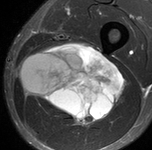
MRI of an extremity soft-tissue mass, one axial slice; position 53 of 90 along the scan axis; STIR; MR volume resampled by the dataset authors to the PET/CT grid (not the native acquisition matrix); 3.27 mm slice thickness; 152 × 150 image matrix, field of view 148 × 146 mm. Male patient. From the clinical record (not read from this slice): histological type: undifferentiated pleomorphic liposarcoma; grade: high; site of the primary tumour: left thigh.
Annotated regions visible in this slice (expert contour drawn on MRI and transferred to this co-registered scan by the dataset authors):
- gross tumour volume including surrounding oedema: bounding box [x1, y1, x2, y2] px = [18, 41, 126, 127]
- gross tumour volume (mass): [20, 41, 126, 127]